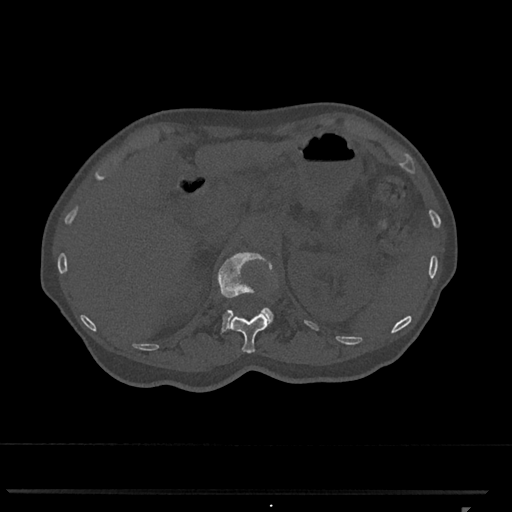
CT including the spine, one axial slice; position 437 of 793 along the scan axis; reconstruction kernel Br40s/3; 120 kVp; bone window (W 1800 / L 400 HU); 0.5 mm slice thickness; 512 × 512 image matrix, field of view 380 × 380 mm. Female patient, age 62 years. From the clinical record (not read from this slice): primary cancer: renal.
Outlined on this slice (semi-automatically segmented with operator editing):
- L1 vertebra: bounding box [x1, y1, x2, y2] px = [218, 252, 273, 333]
- T12 vertebra: [228, 254, 278, 353]